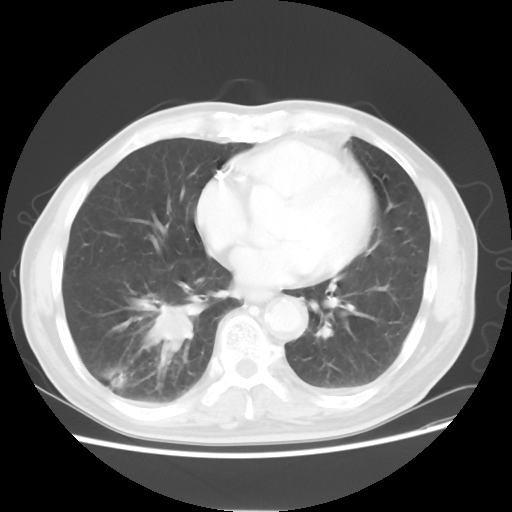
Chest CT, one axial slice; position 23 of 58 along the scan axis; lung window (W 1500 / L -600 HU); 5 mm slice thickness; 512 × 512 image matrix, field of view 360 × 360 mm. Patient: male, 74 years. From the clinical record (not read from this slice): clinical TNM (as recorded): T1c N1 M1.
Structures marked on this image (bounding box drawn by a radiologist):
- lung tumour (recorded histology: adenocarcinoma): bounding box [x1, y1, x2, y2] px = [127, 291, 201, 370]